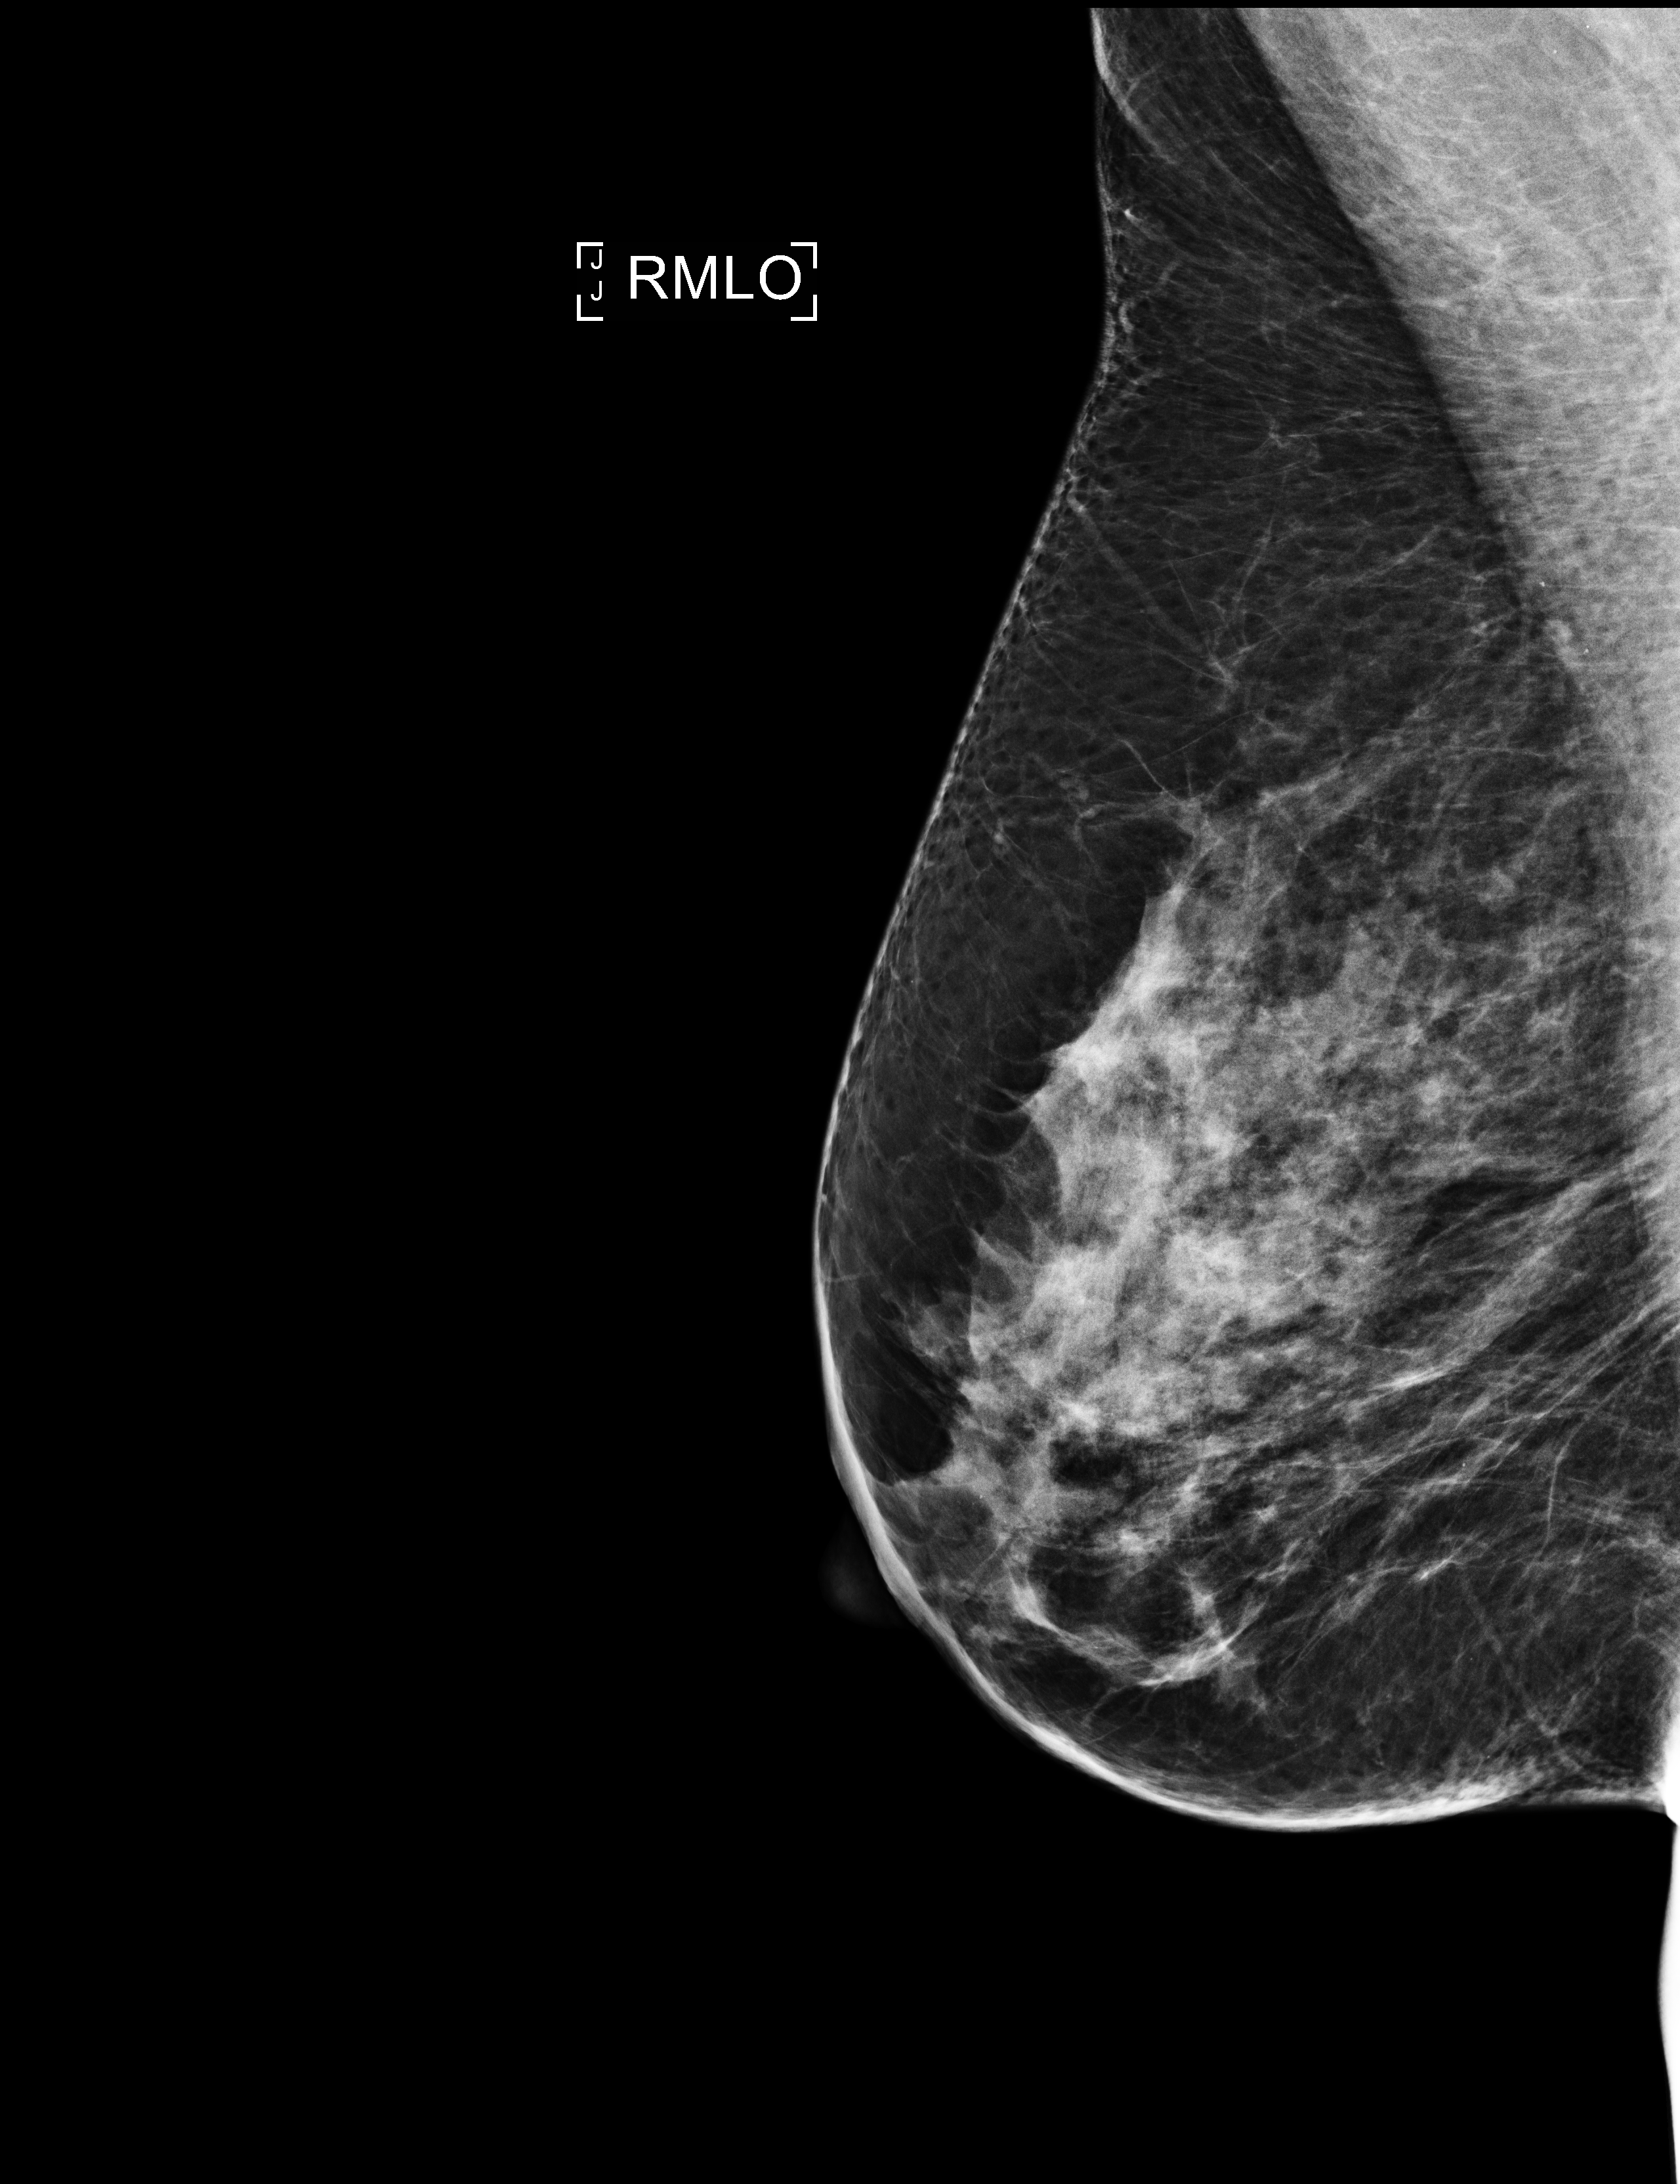
Annual screening mammography examination. Patient: female, 55 years.
Image type: full-field digital mammogram. Breast: right. Projection: medio-lateral oblique projection. Breast density at the screening exam (both breasts): heterogeneously dense (BI-RADS density category c). Final BI-RADS category for the screening round (tomosynthesis exam, both breasts): category 2. Recall: no recall after this screen.